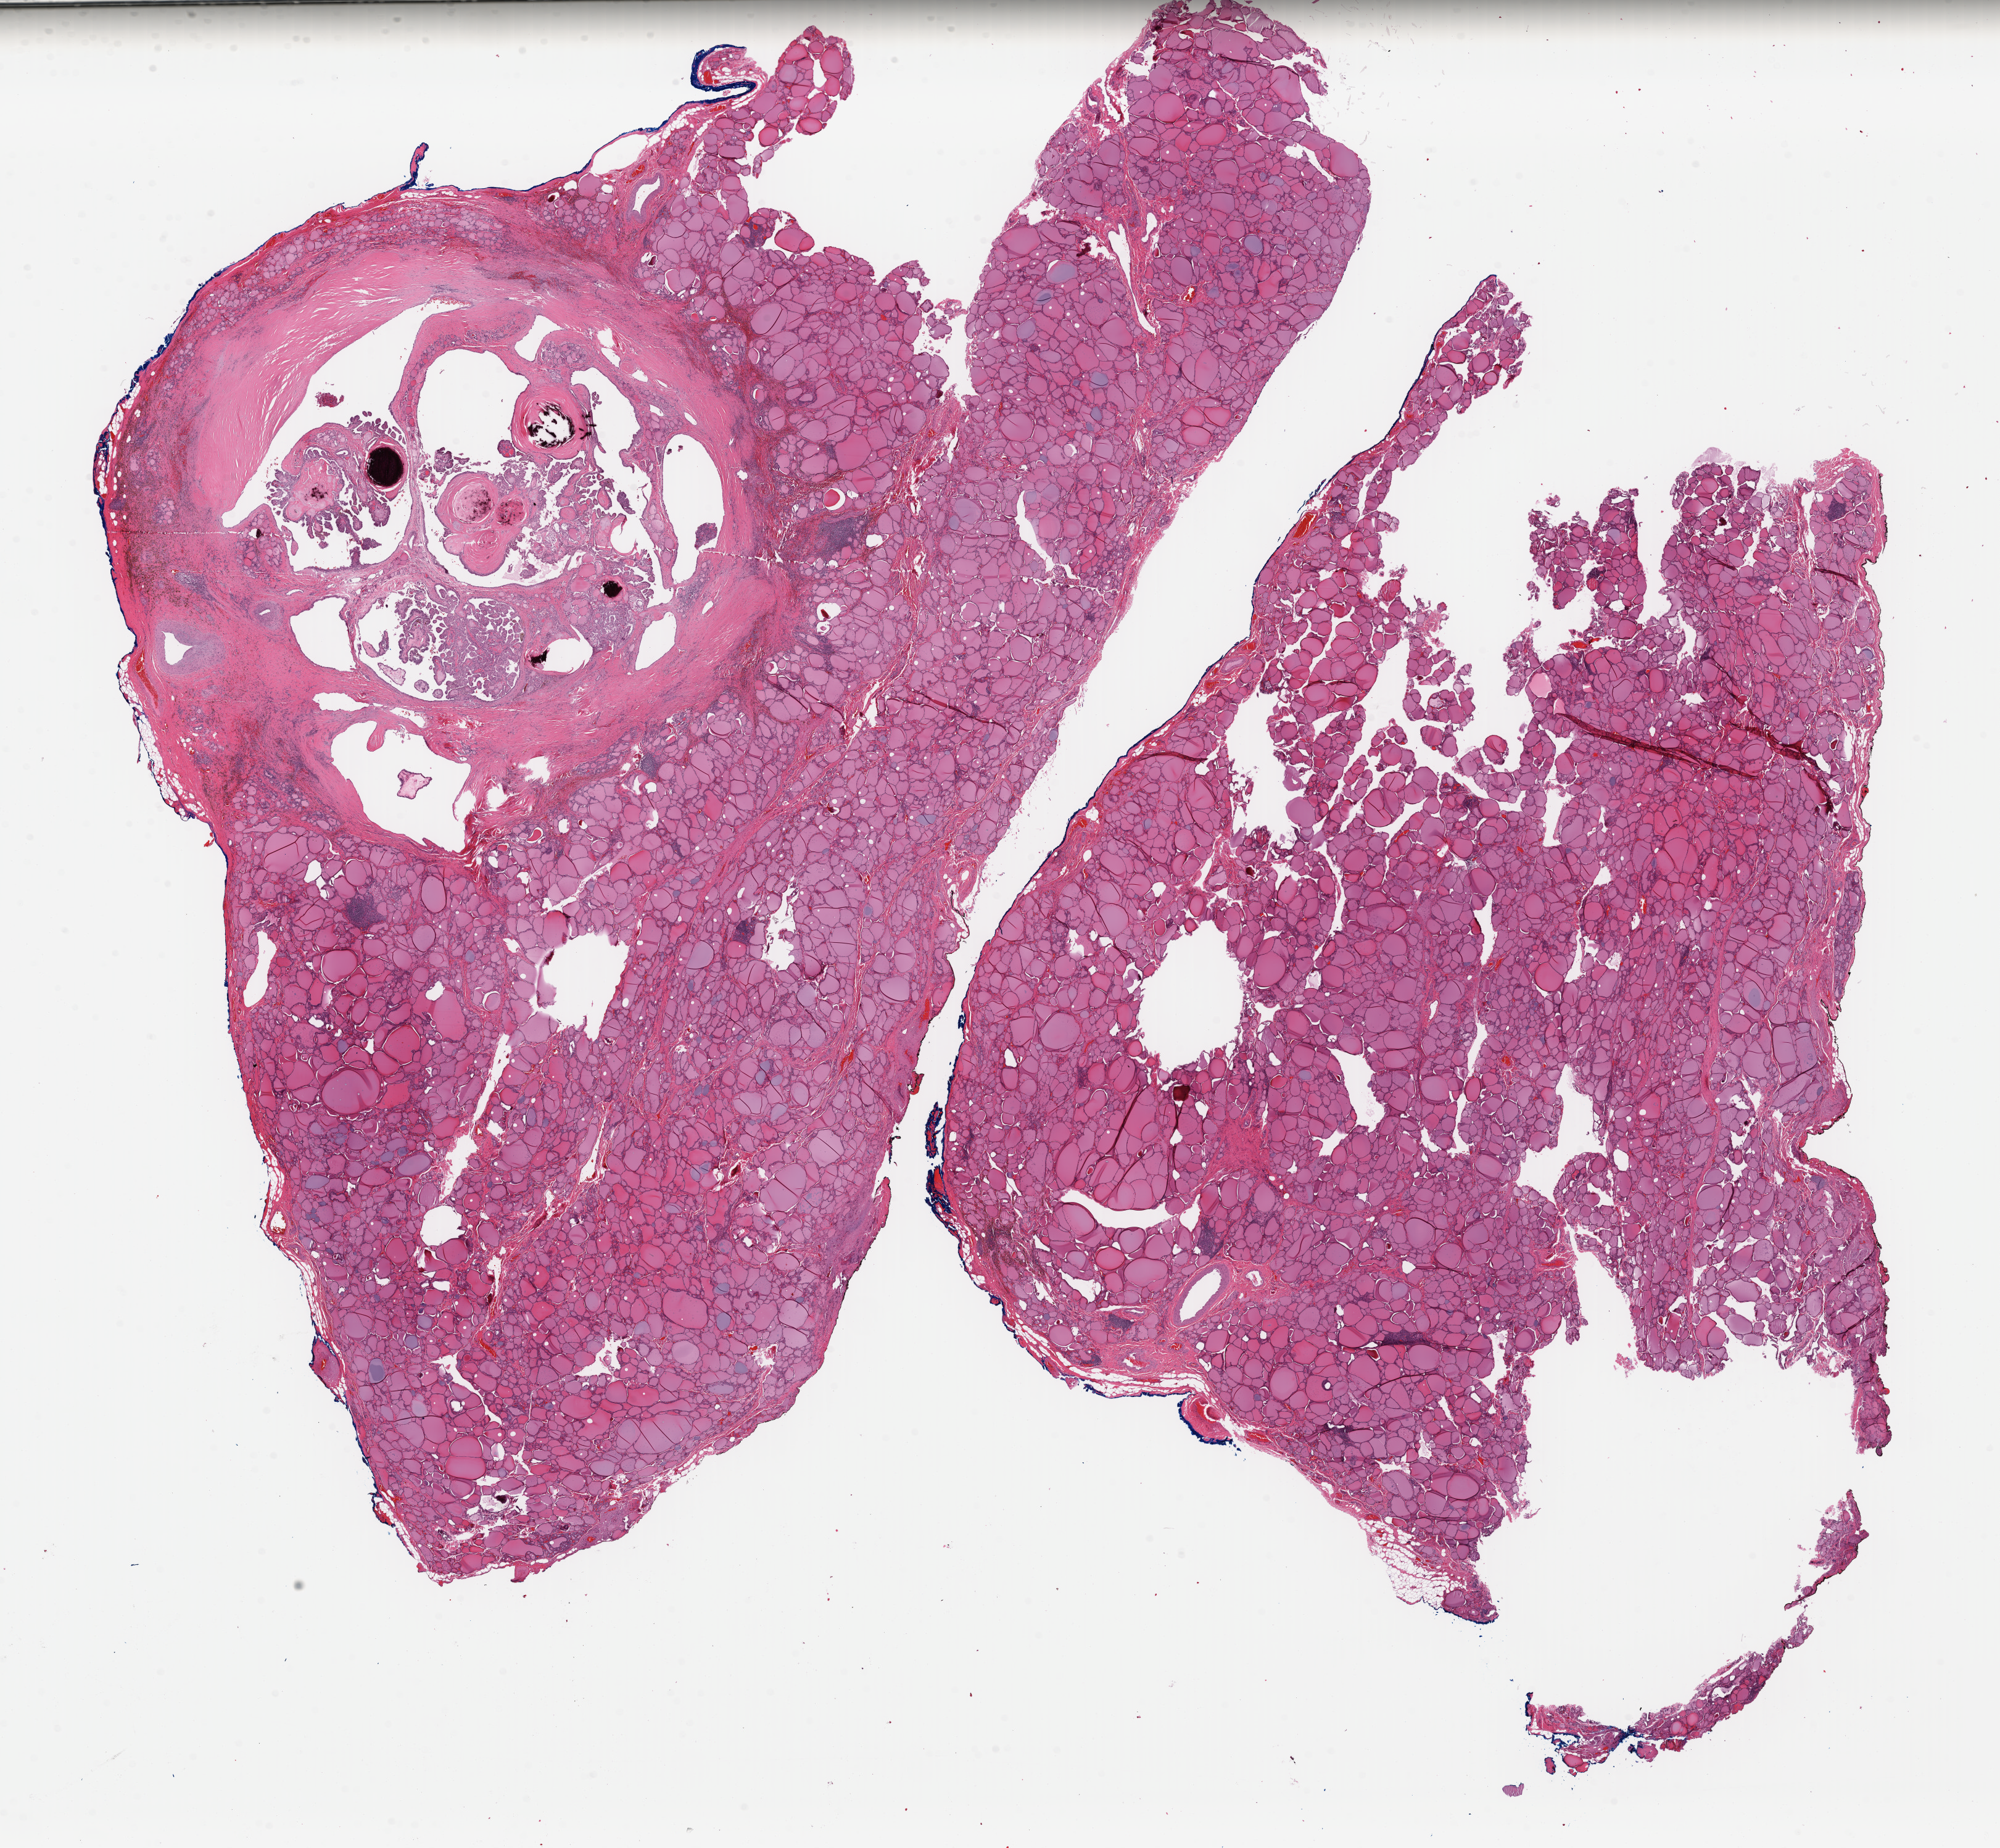
Whole-slide histology image, H&E-stained, low-resolution overview of the scanned area, about 25.6 x 23.6 mm (acquisition: 40x scan); formalin-fixed paraffin-embedded (FFPE) diagnostic section; primary tumour sample from the thyroid. Patient: female, age at initial diagnosis 45 years.
Lymph nodes positive (case pathology): 0 of 3 examined. TNM: T1b N0 M0. Diagnosis: Papillary adenocarcinoma, NOS. AJCC pathologic stage: I.